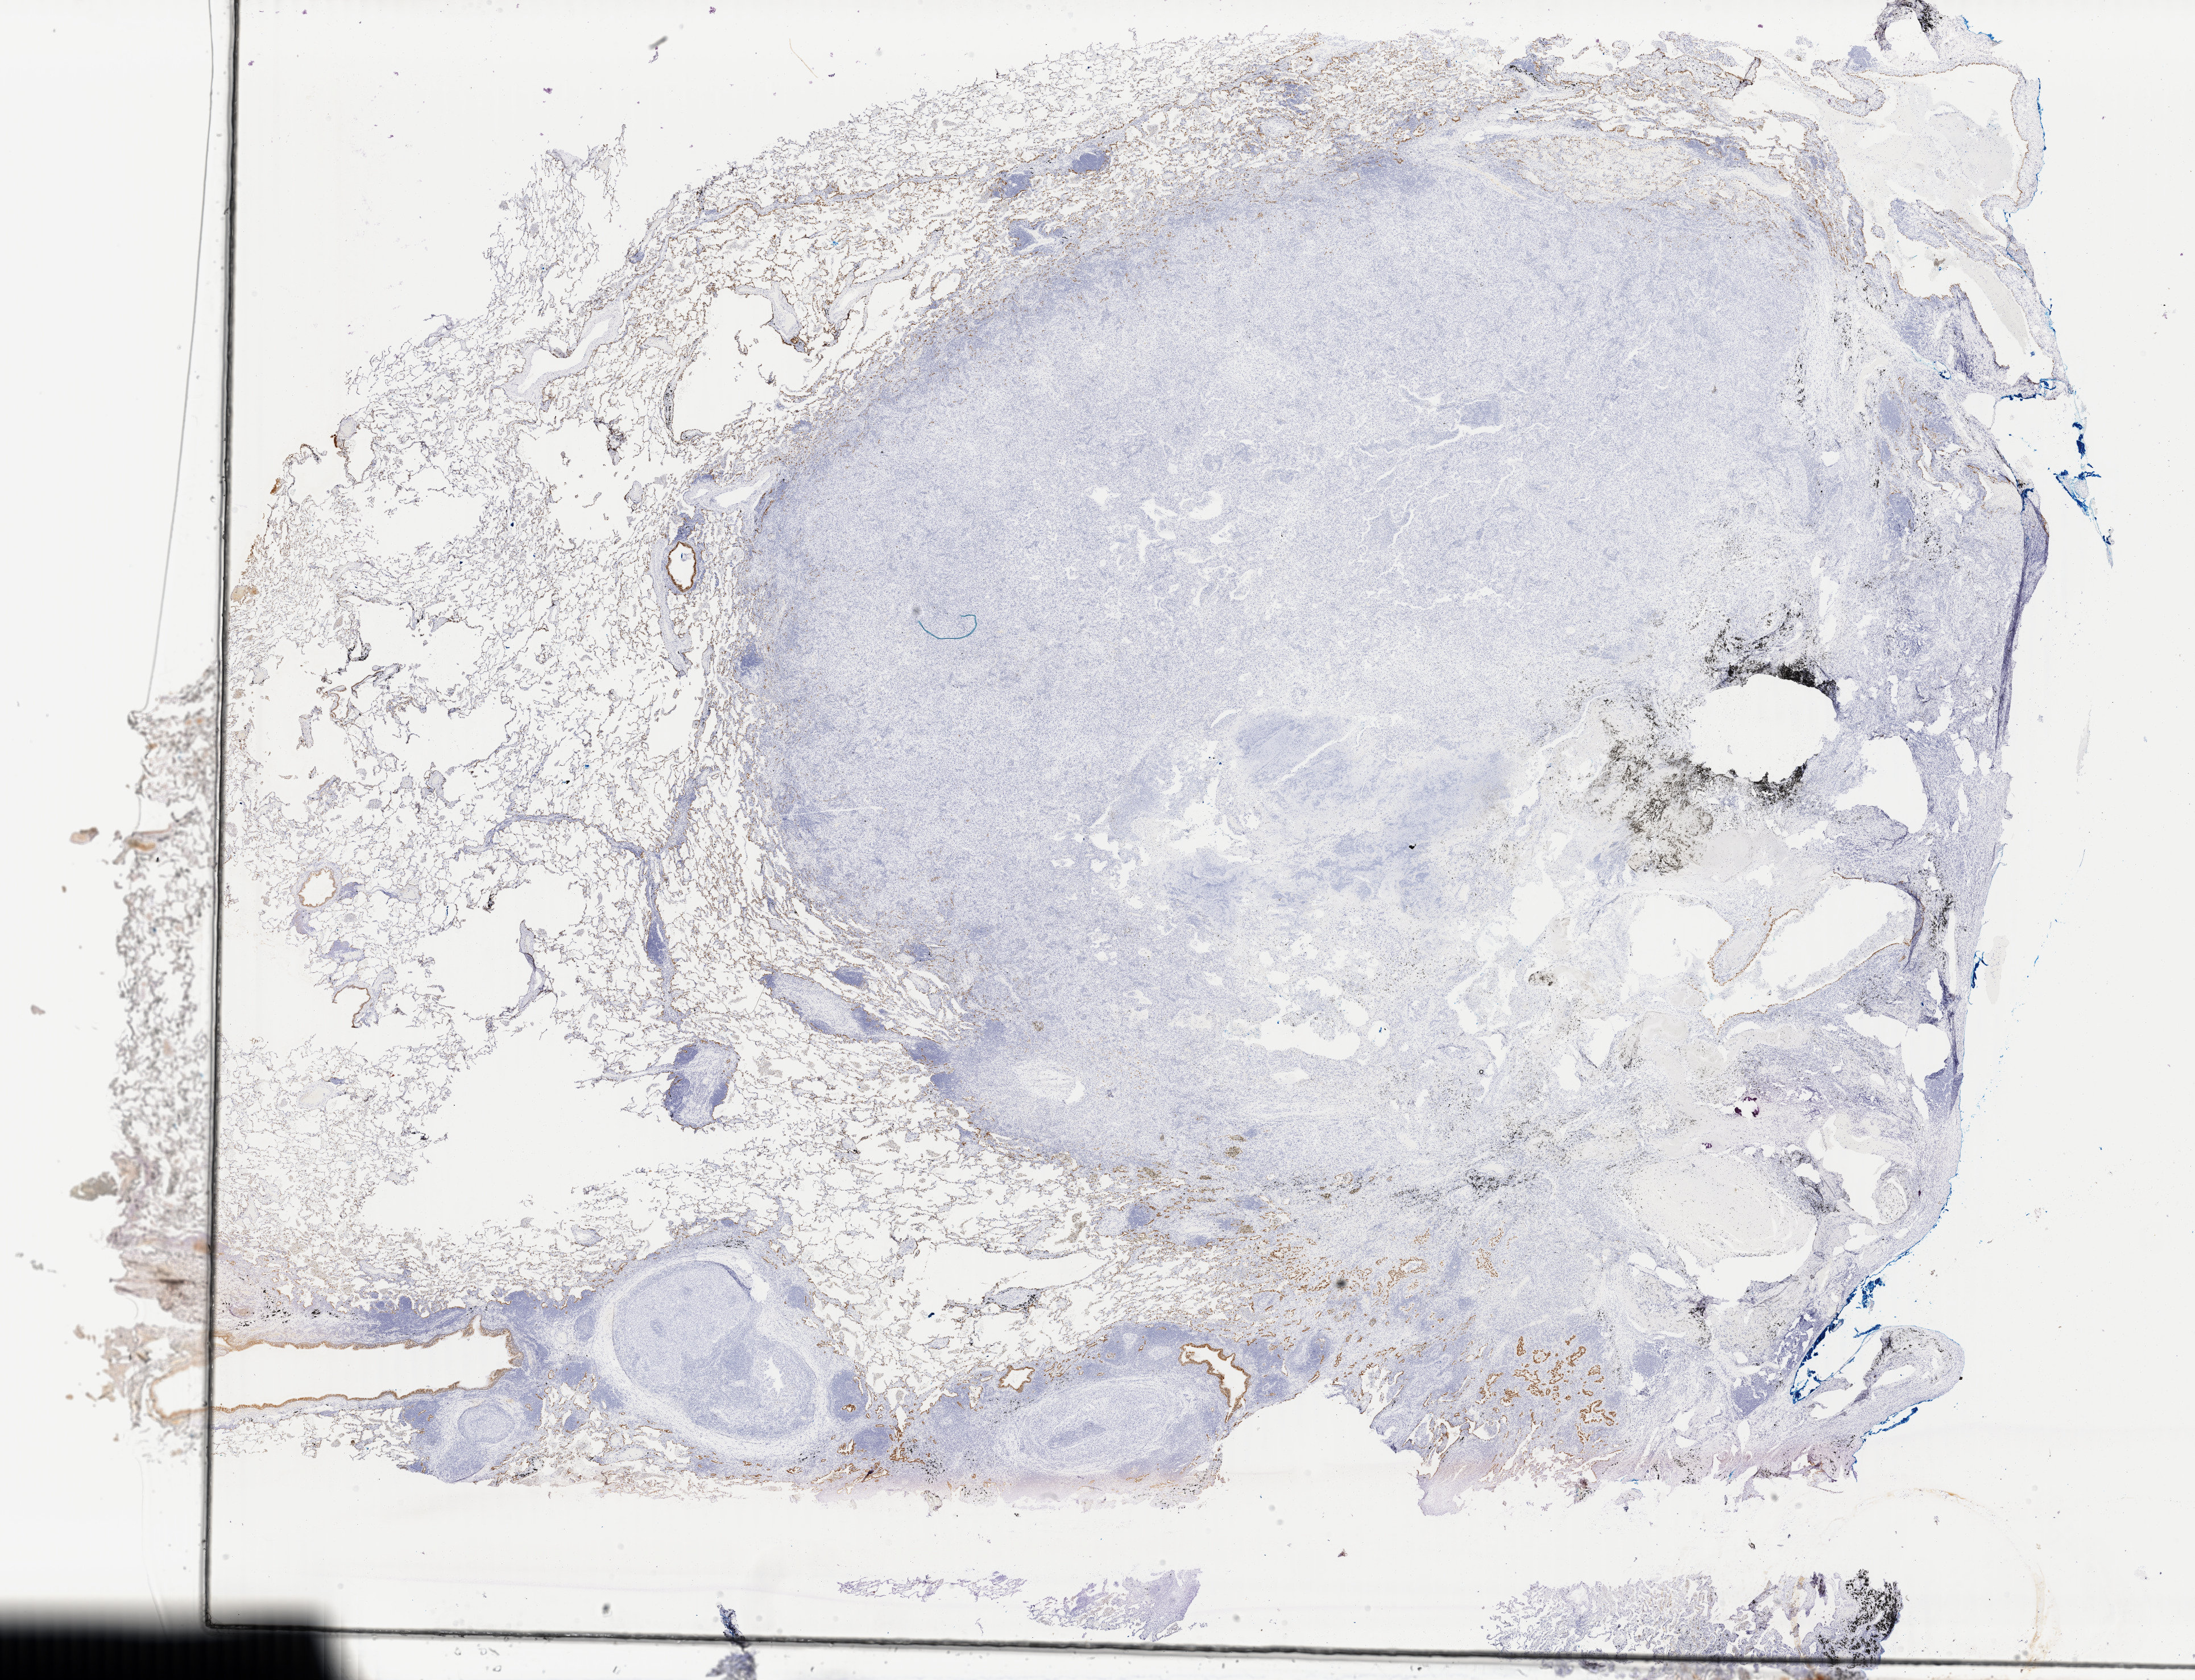
Immunohistochemistry (IHC) whole-slide image stained for TTF-1 (thyroid transcription factor 1), a low-resolution overview of the entire scanned area, about 30.7 x 23.5 mm, specimen: tumor tissue, anatomic site: lung (right). Patient: male, age 59 years.
• histologic diagnosis: Adenosquamous carcinoma